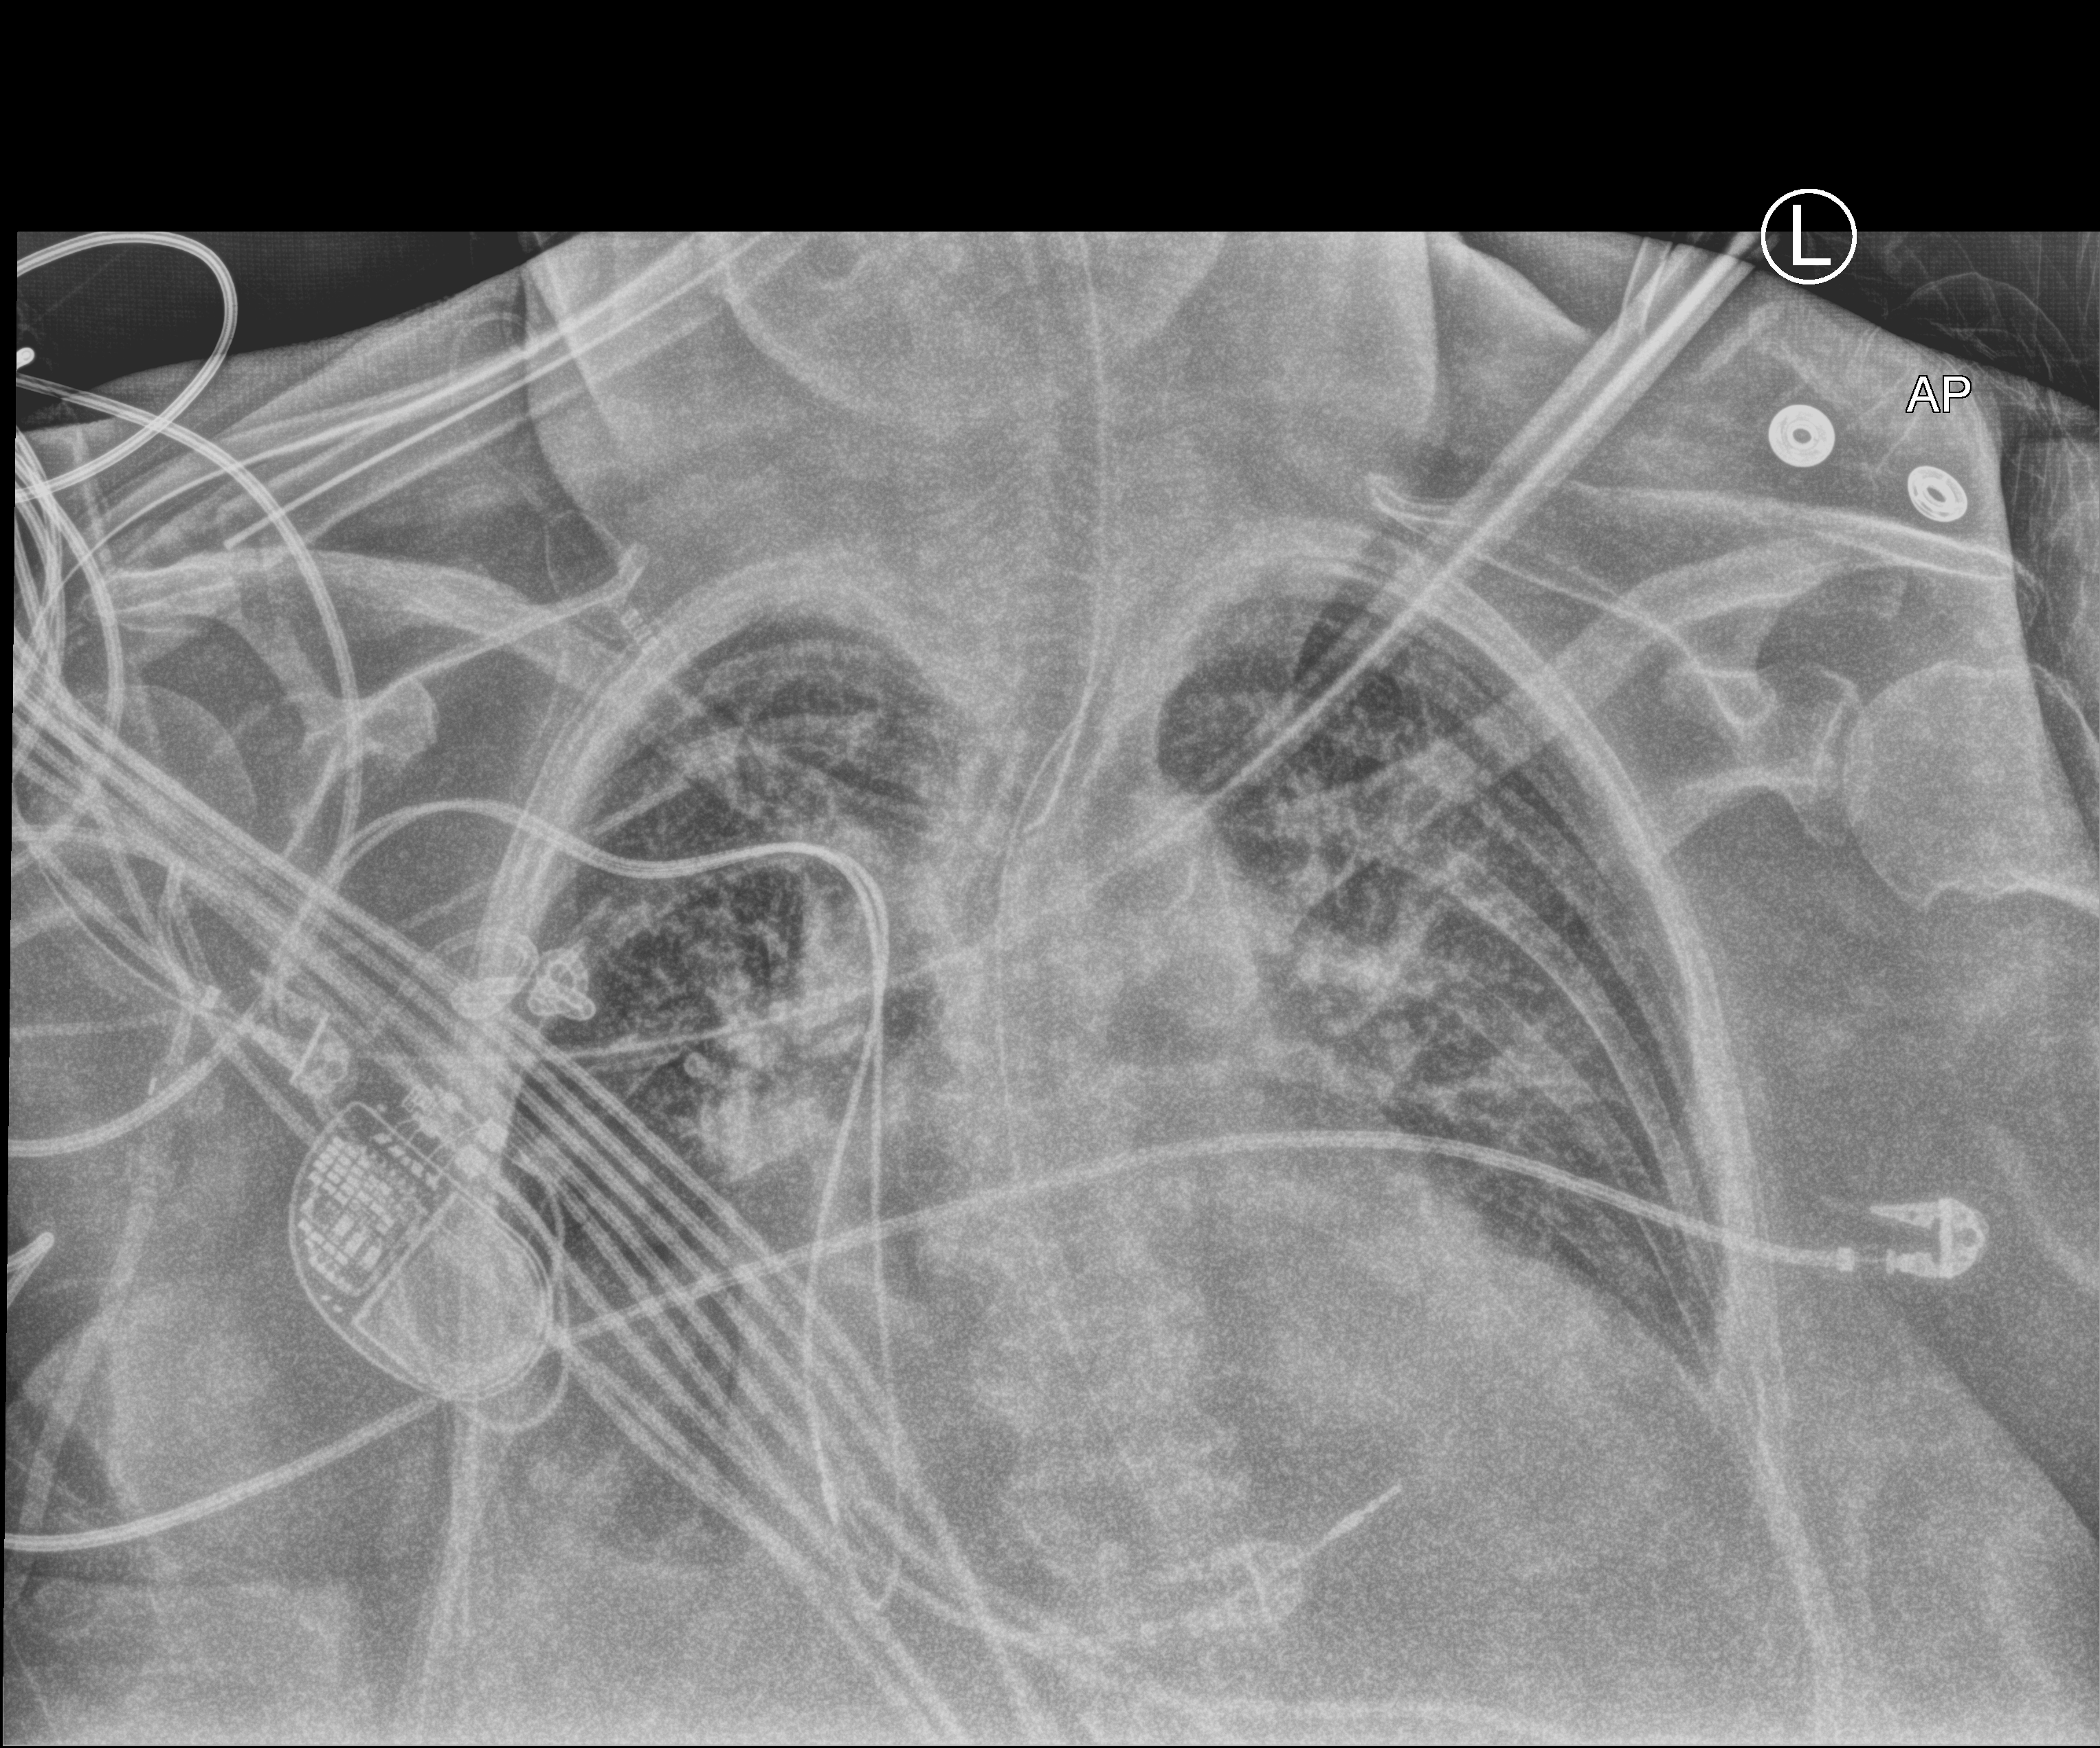
Chest X-ray (portable); anteroposterior (AP) projection. Female patient hospitalised with COVID-19, age 75–90 years.
From the hospital-stay record, not from the radiograph (when in the stay this image was taken is not recorded):
- admitted to intensive care during this hospital stay: yes
- mechanically ventilated during this hospital stay: yes